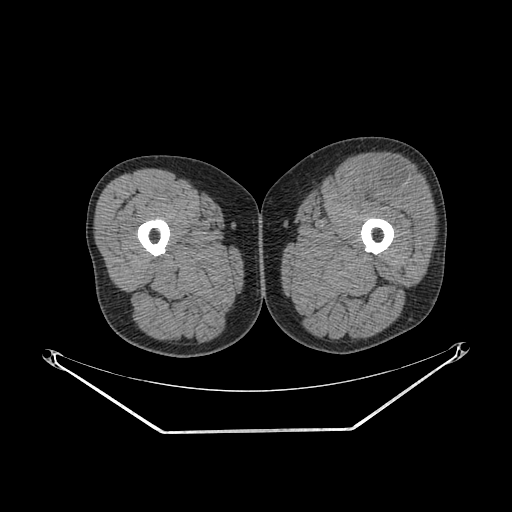
CT of an extremity soft-tissue mass (from a PET/CT study), one axial slice. Position 227 of 267 along the scan axis. Reconstruction kernel SOFT. Soft-tissue window (W 400 / L 40 HU). 512 × 512 image matrix, field of view 500 × 500 mm. Male patient. Case-level facts recorded for this patient, not image findings: histological type: extraskeletal osteosarcoma; grade: high; site of the primary tumour: thigh.
Outlined on this slice (expert contour drawn on MRI and transferred to this co-registered scan by the dataset authors):
- gross tumour volume (mass): bounding box <365,164,423,209> (left, top, right, bottom; pixels)